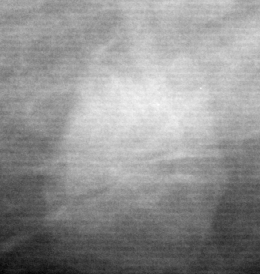
Cropped region of a digitized screen-film mammogram centred on a radiologist-marked abnormality; right breast; MLO view.
- Marked abnormality: mass, shape oval, margins circumscribed; BI-RADS assessment category 4; subtlety rating 5 on a 1 (subtle) to 5 (obvious) scale; pathology (as recorded): benign.